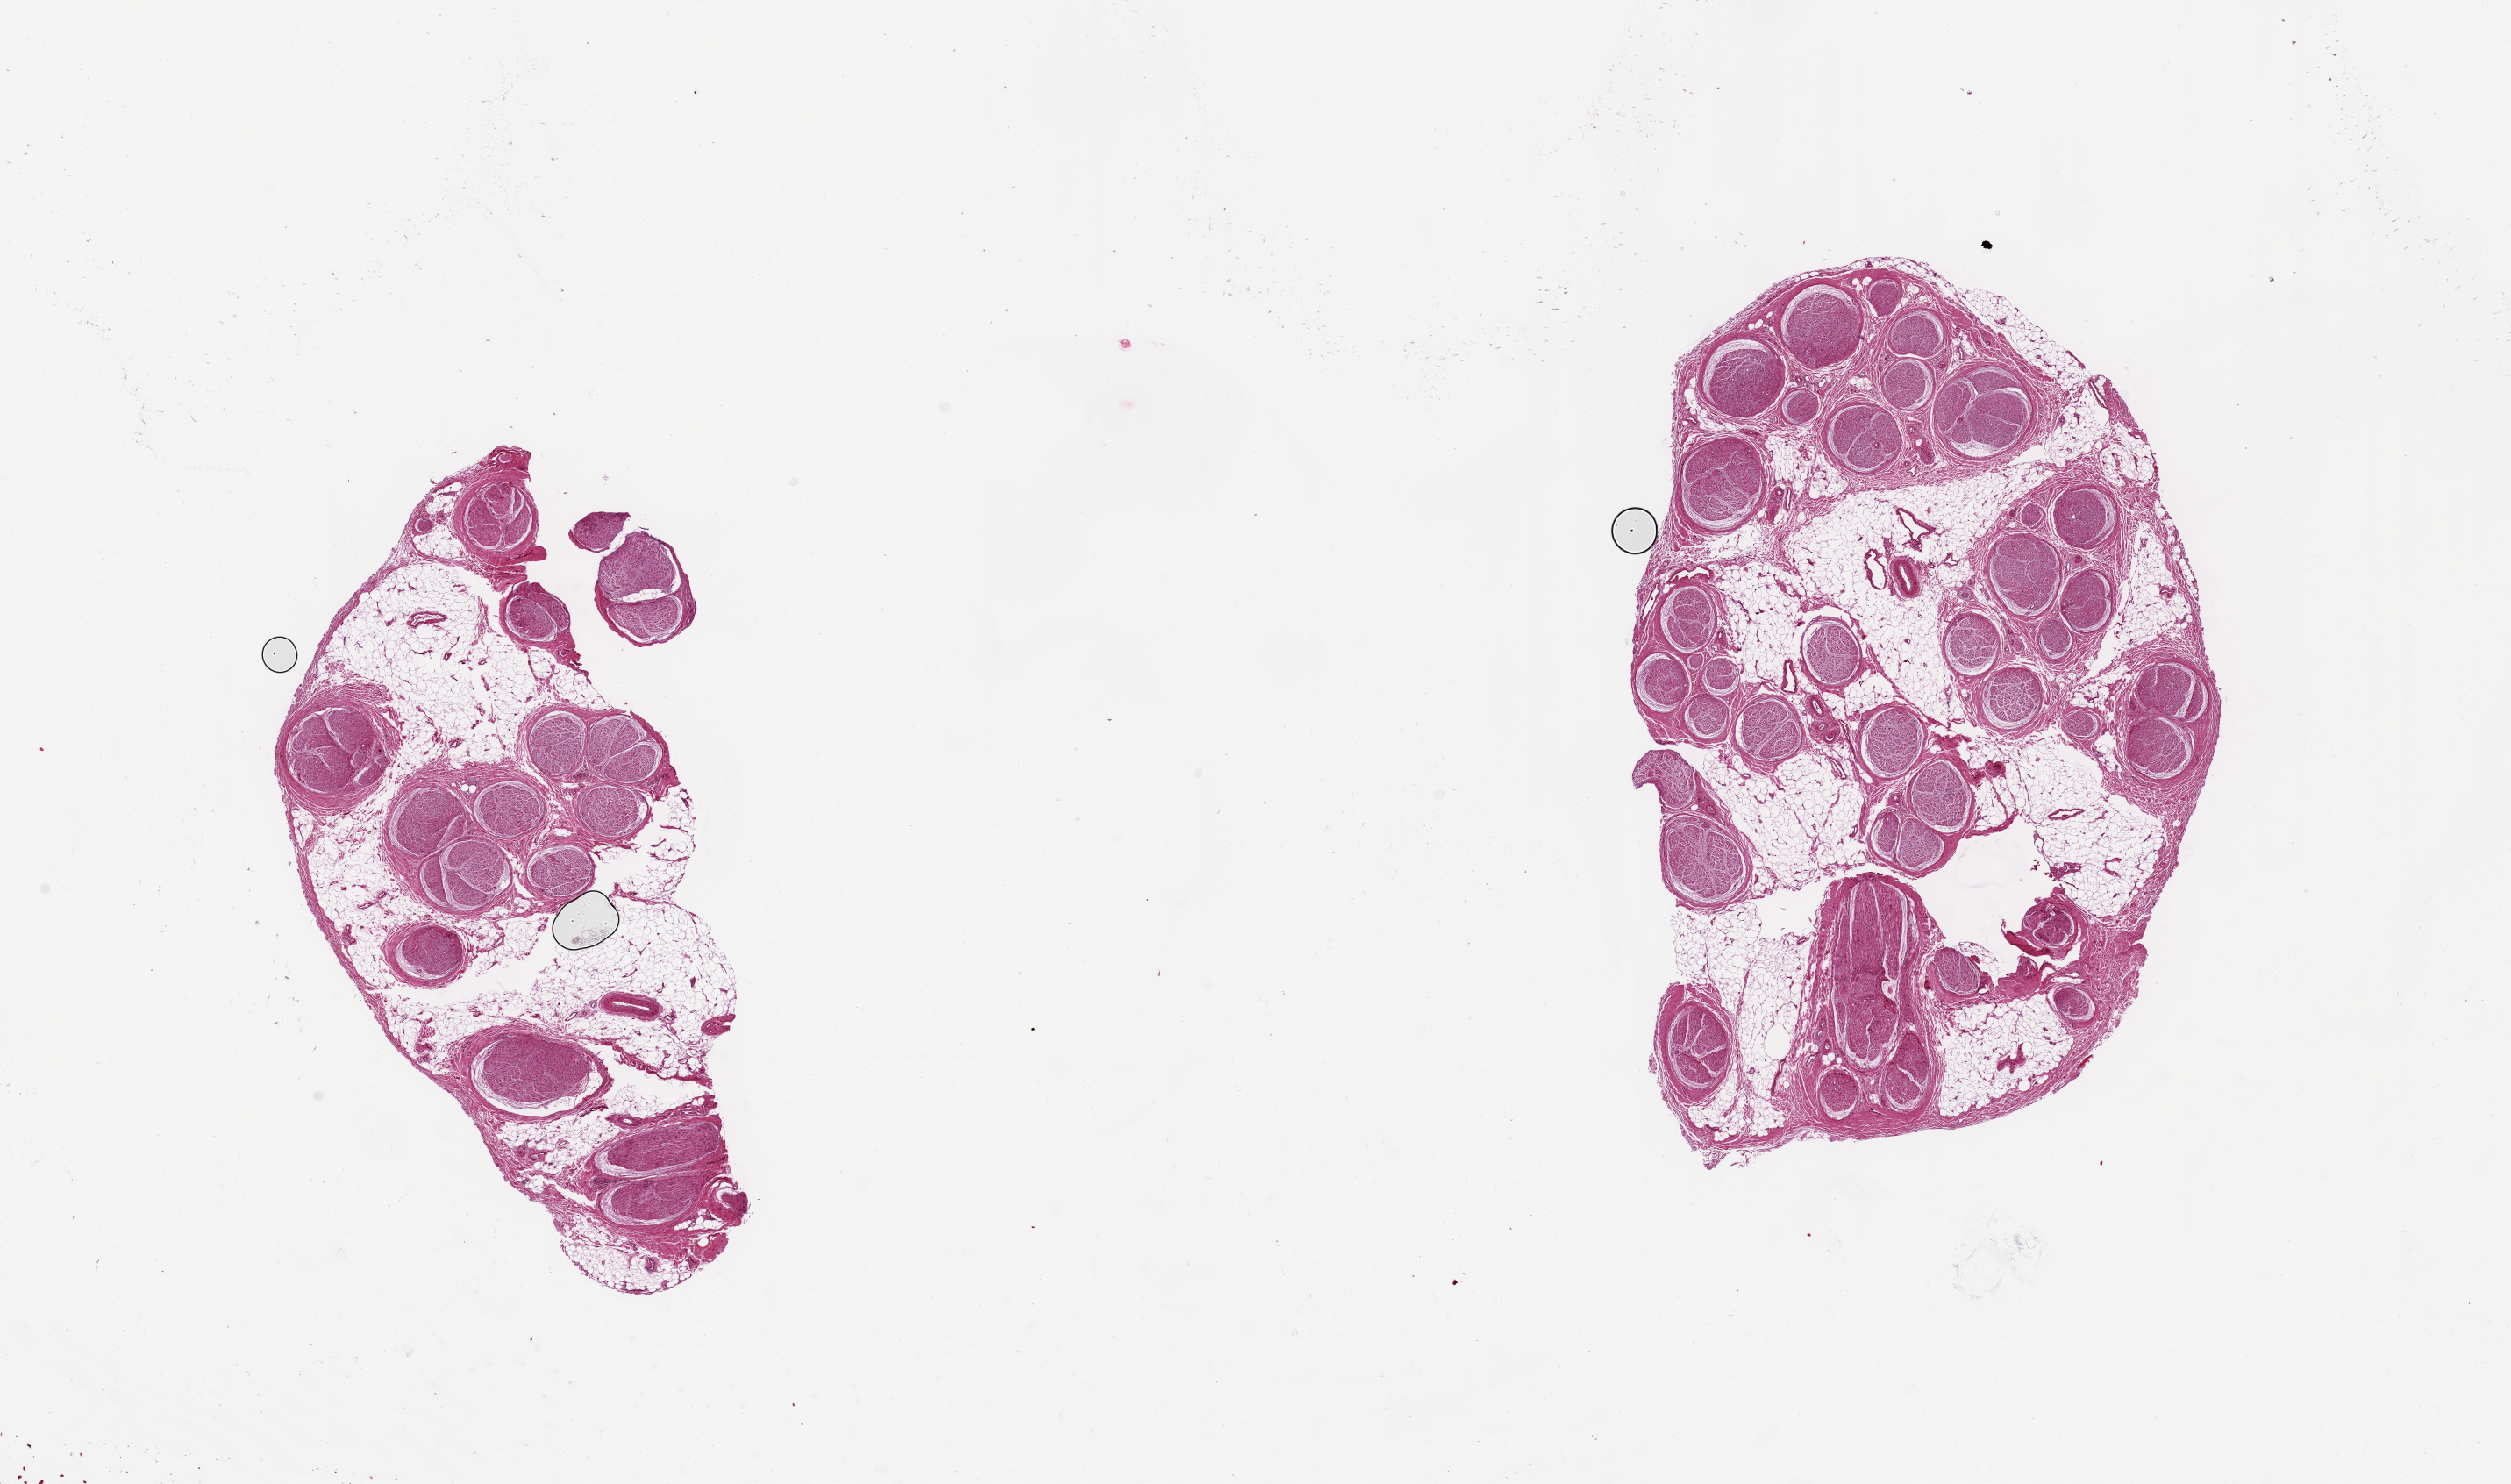
Whole-slide image, H&E stain, whole scanned area (about 22.6 x 13.4 mm, from a 20x scan) shown as a low-resolution overview. PAXgene-fixed, paraffin-embedded tissue. Sampled site (target tissue): tibial nerve. Tissue donor sample. Donor sex: male.
- review note (as recorded): Approximately 40% of specimen is intermingled adipose tissue